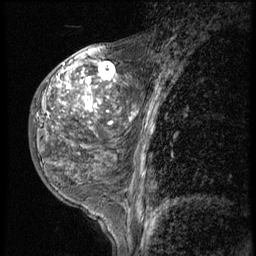
Breast MRI (dynamic contrast-enhanced), one sagittal slice; slice 19 of 56 in the series (ordered by position); 3 images stored at this slice position (order not interpretable as contrast timing); 1.5 T; TE 4.2 ms, TR 9 ms; 2.5 mm slice thickness; 256 × 256 image matrix, field of view 180 × 180 mm. Patient: female, 50 years. Case-level facts recorded for this patient, not image findings: setting: breast cancer imaged before/during neoadjuvant chemotherapy; receptor status: triple-negative.
Outlined on this slice (semi-automatically segmented with operator editing):
- analysis volume of interest (the breast-tissue region the enhancement analysis was run in; not a lesion): bounding box [x1, y1, x2, y2] px = [28, 50, 117, 191]
- tumour enhancement mask (voxels above the 140 % enhancement threshold inside the analysis volume of interest): [47, 62, 115, 125]